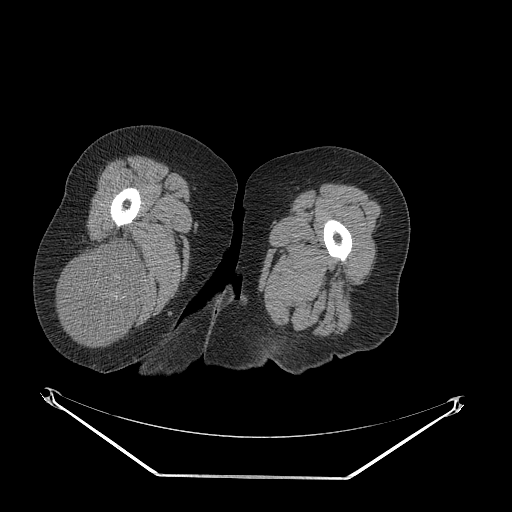
CT of an extremity soft-tissue mass (from a PET/CT study), one axial slice. Position 39 of 257 along the scan axis. Reconstruction kernel STANDARD. 140 kVp. Soft-tissue window (W 400 / L 40 HU). 512 × 512 image matrix, field of view 500 × 500 mm. Female patient. From the clinical record (not read from this slice): histological type: synovial sarcoma; grade: intermediate; site of the primary tumour: right buttock.
Annotated regions visible in this slice (expert contour drawn on MRI and transferred to this co-registered scan by the dataset authors):
- gross tumour volume including surrounding oedema: bounding box [x1, y1, x2, y2] px = [62, 244, 143, 341]
- gross tumour volume (mass): [62, 244, 143, 341]